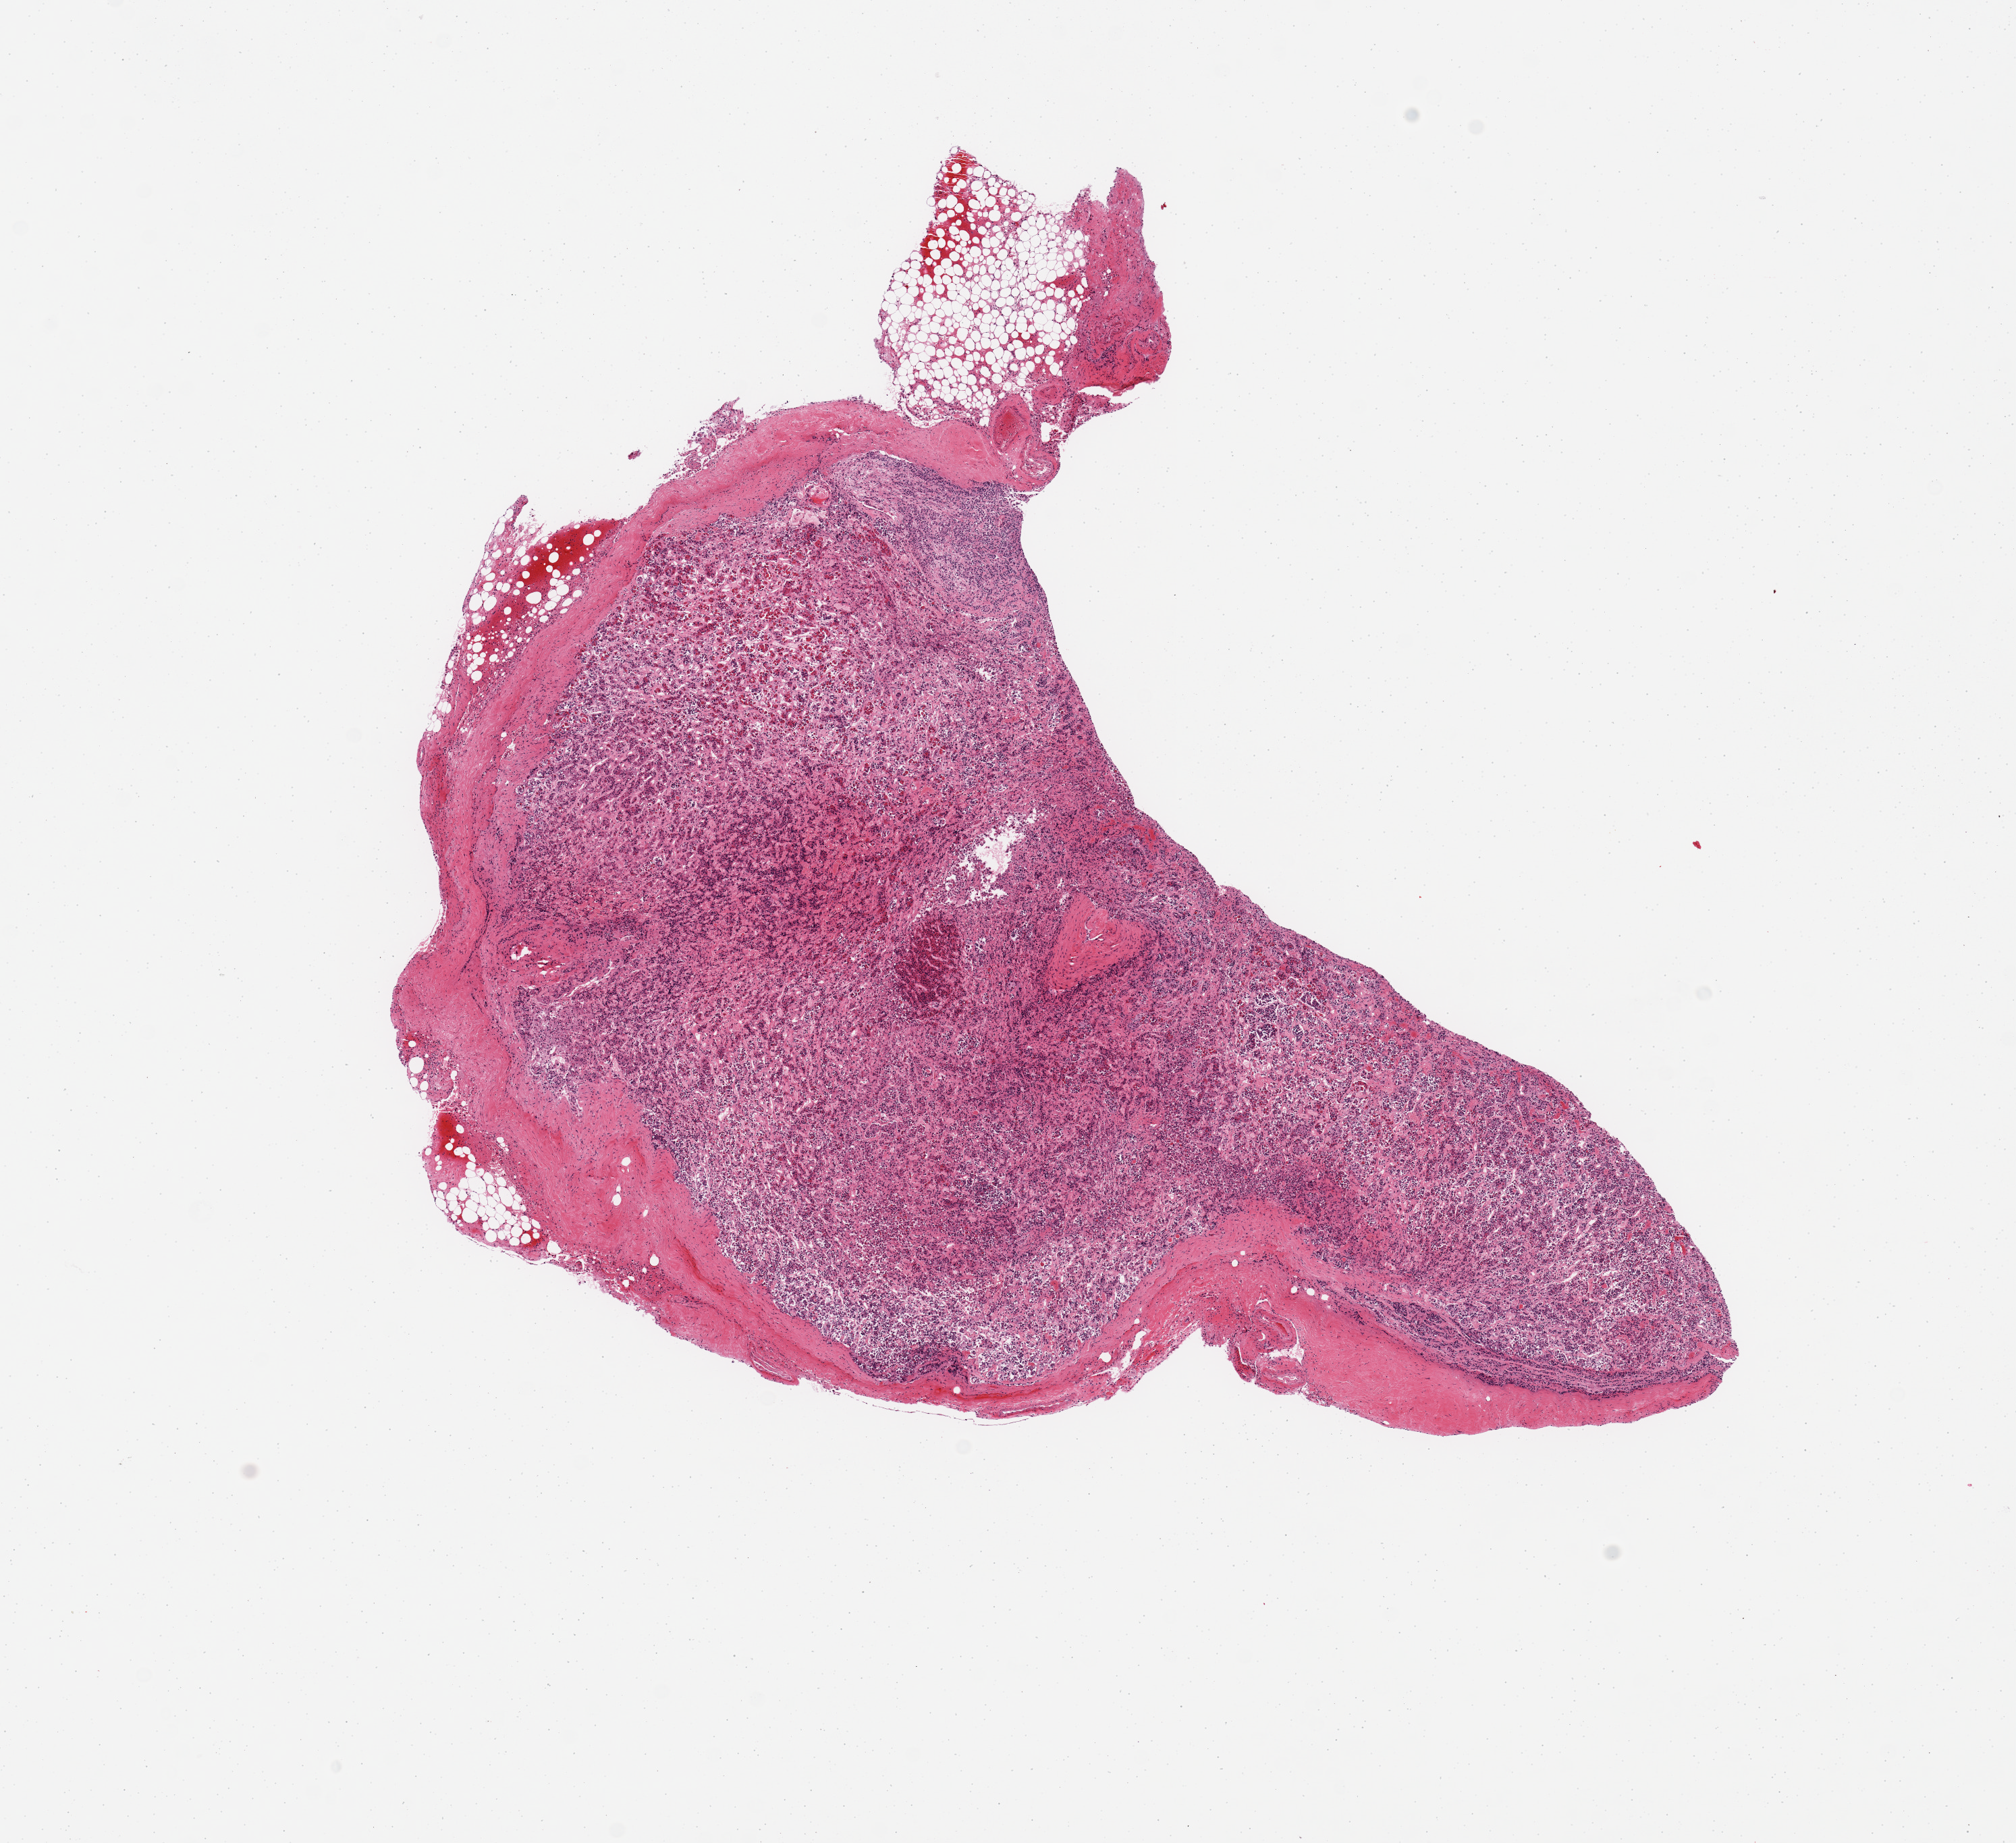
Haematoxylin and eosin whole-slide image — low-resolution overview of the scanned area, about 11.8 x 10.8 mm (from a 20x scan). PAXgene-fixed, paraffin-embedded tissue. Target tissue: pituitary. Donor tissue sample.
Review note (as recorded): 1 piece, predominantly adenohypophysis with minute focus of neurohypophysis.